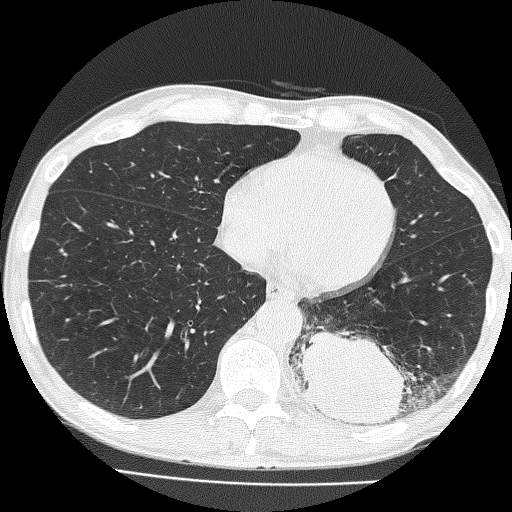
Low-dose screening chest CT, one axial slice. Slice 57 of 160 in the series (ordered by position). Reconstruction kernel FC51. 120 kVp. Lung window (W 1500 / L -600 HU). 2 mm slice thickness. 512 × 512 image matrix, field of view 324 × 324 mm.
Outlined on this slice (manually delineated by an expert):
- lesion 1 (tumor, lower lobe of left lung): box from (x=294, y=328) to (x=408, y=426) px